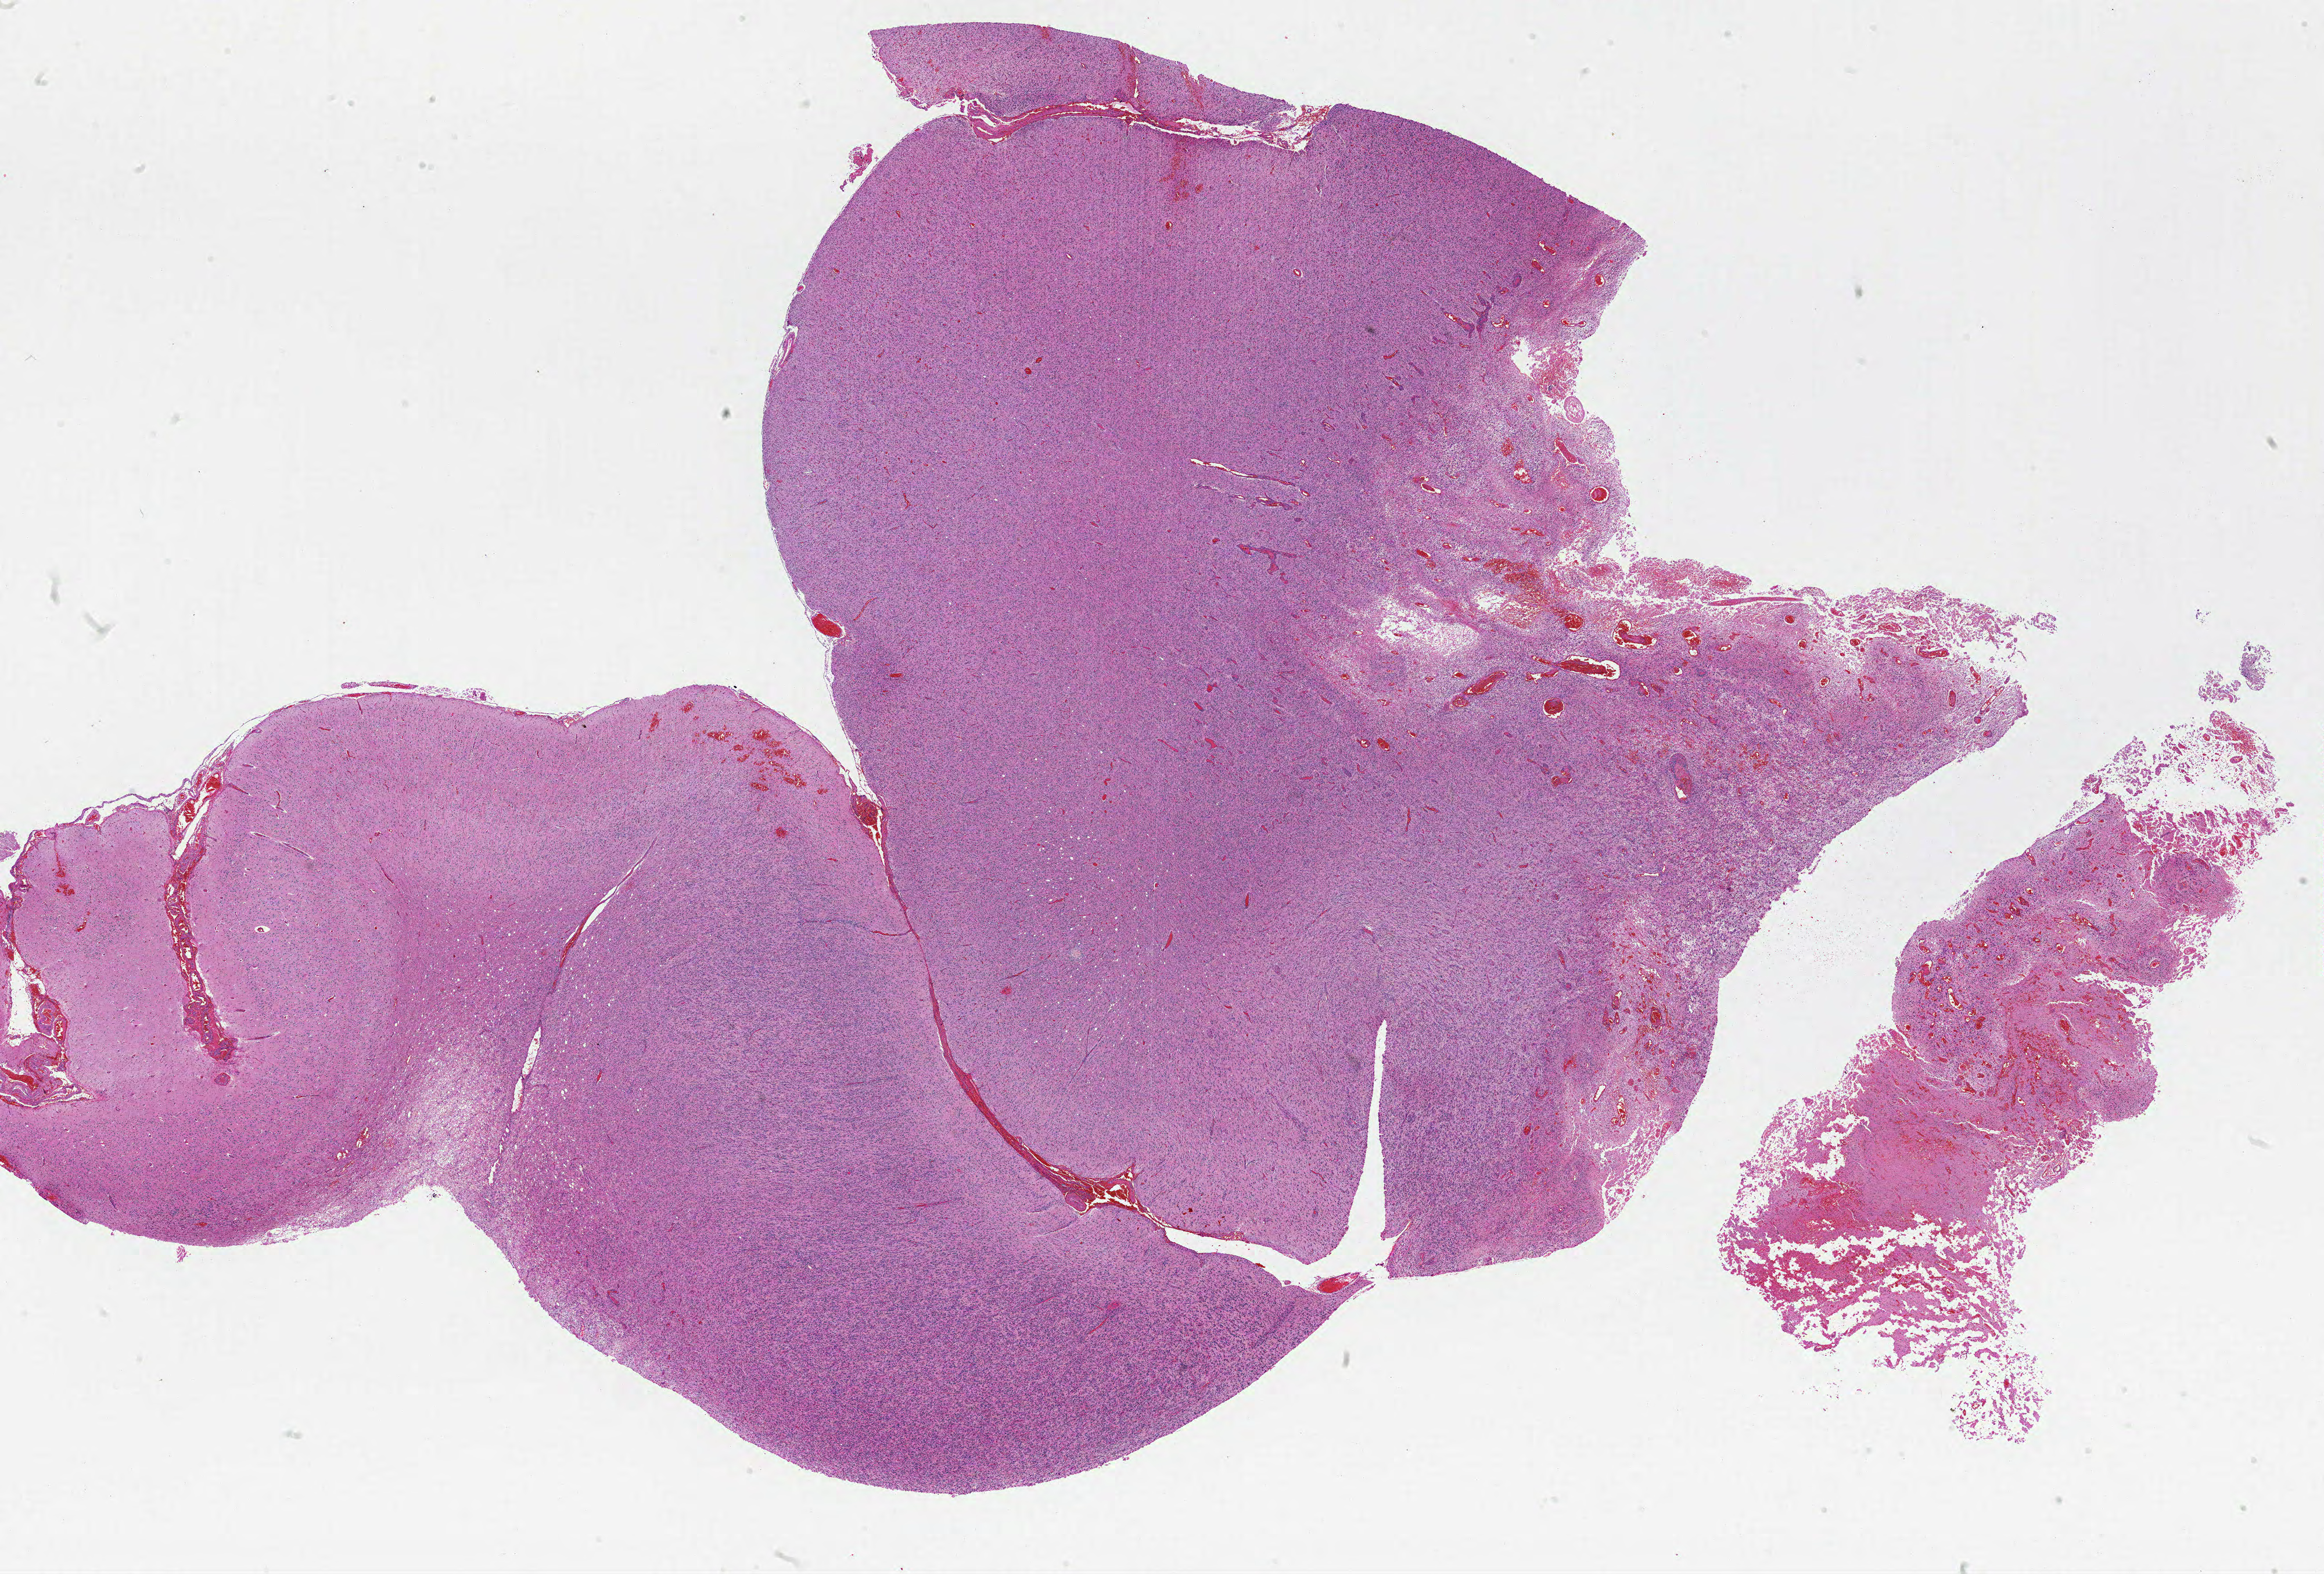
Digitized Hematoxylin and eosin (H&E) stained tissue section (whole slide), low-resolution overview of the scanned area, about 32.0 x 21.6 mm, formalin-fixed paraffin-embedded (FFPE) diagnostic section, primary tumour sample from the brain. Patient: male, age at initial diagnosis 55 years.
Histologic diagnosis: Glioblastoma.